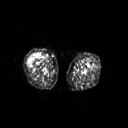
FDG PET of an extremity soft-tissue mass (from a PET/CT study), one axial slice. Position 209 of 311 along the scan axis. 128 × 128 image matrix, field of view 500 × 500 mm. Female patient, age 57 years. Case-level facts recorded for this patient, not image findings: histological type: pleiomorphic undifferentiated sarcoma; grade: high; site of the primary tumour: right quadricep.
Annotated regions visible in this slice (expert contour drawn on MRI and transferred to this co-registered scan by the dataset authors):
- tumour plus oedema (research contour): box from (x=33, y=53) to (x=40, y=57) px